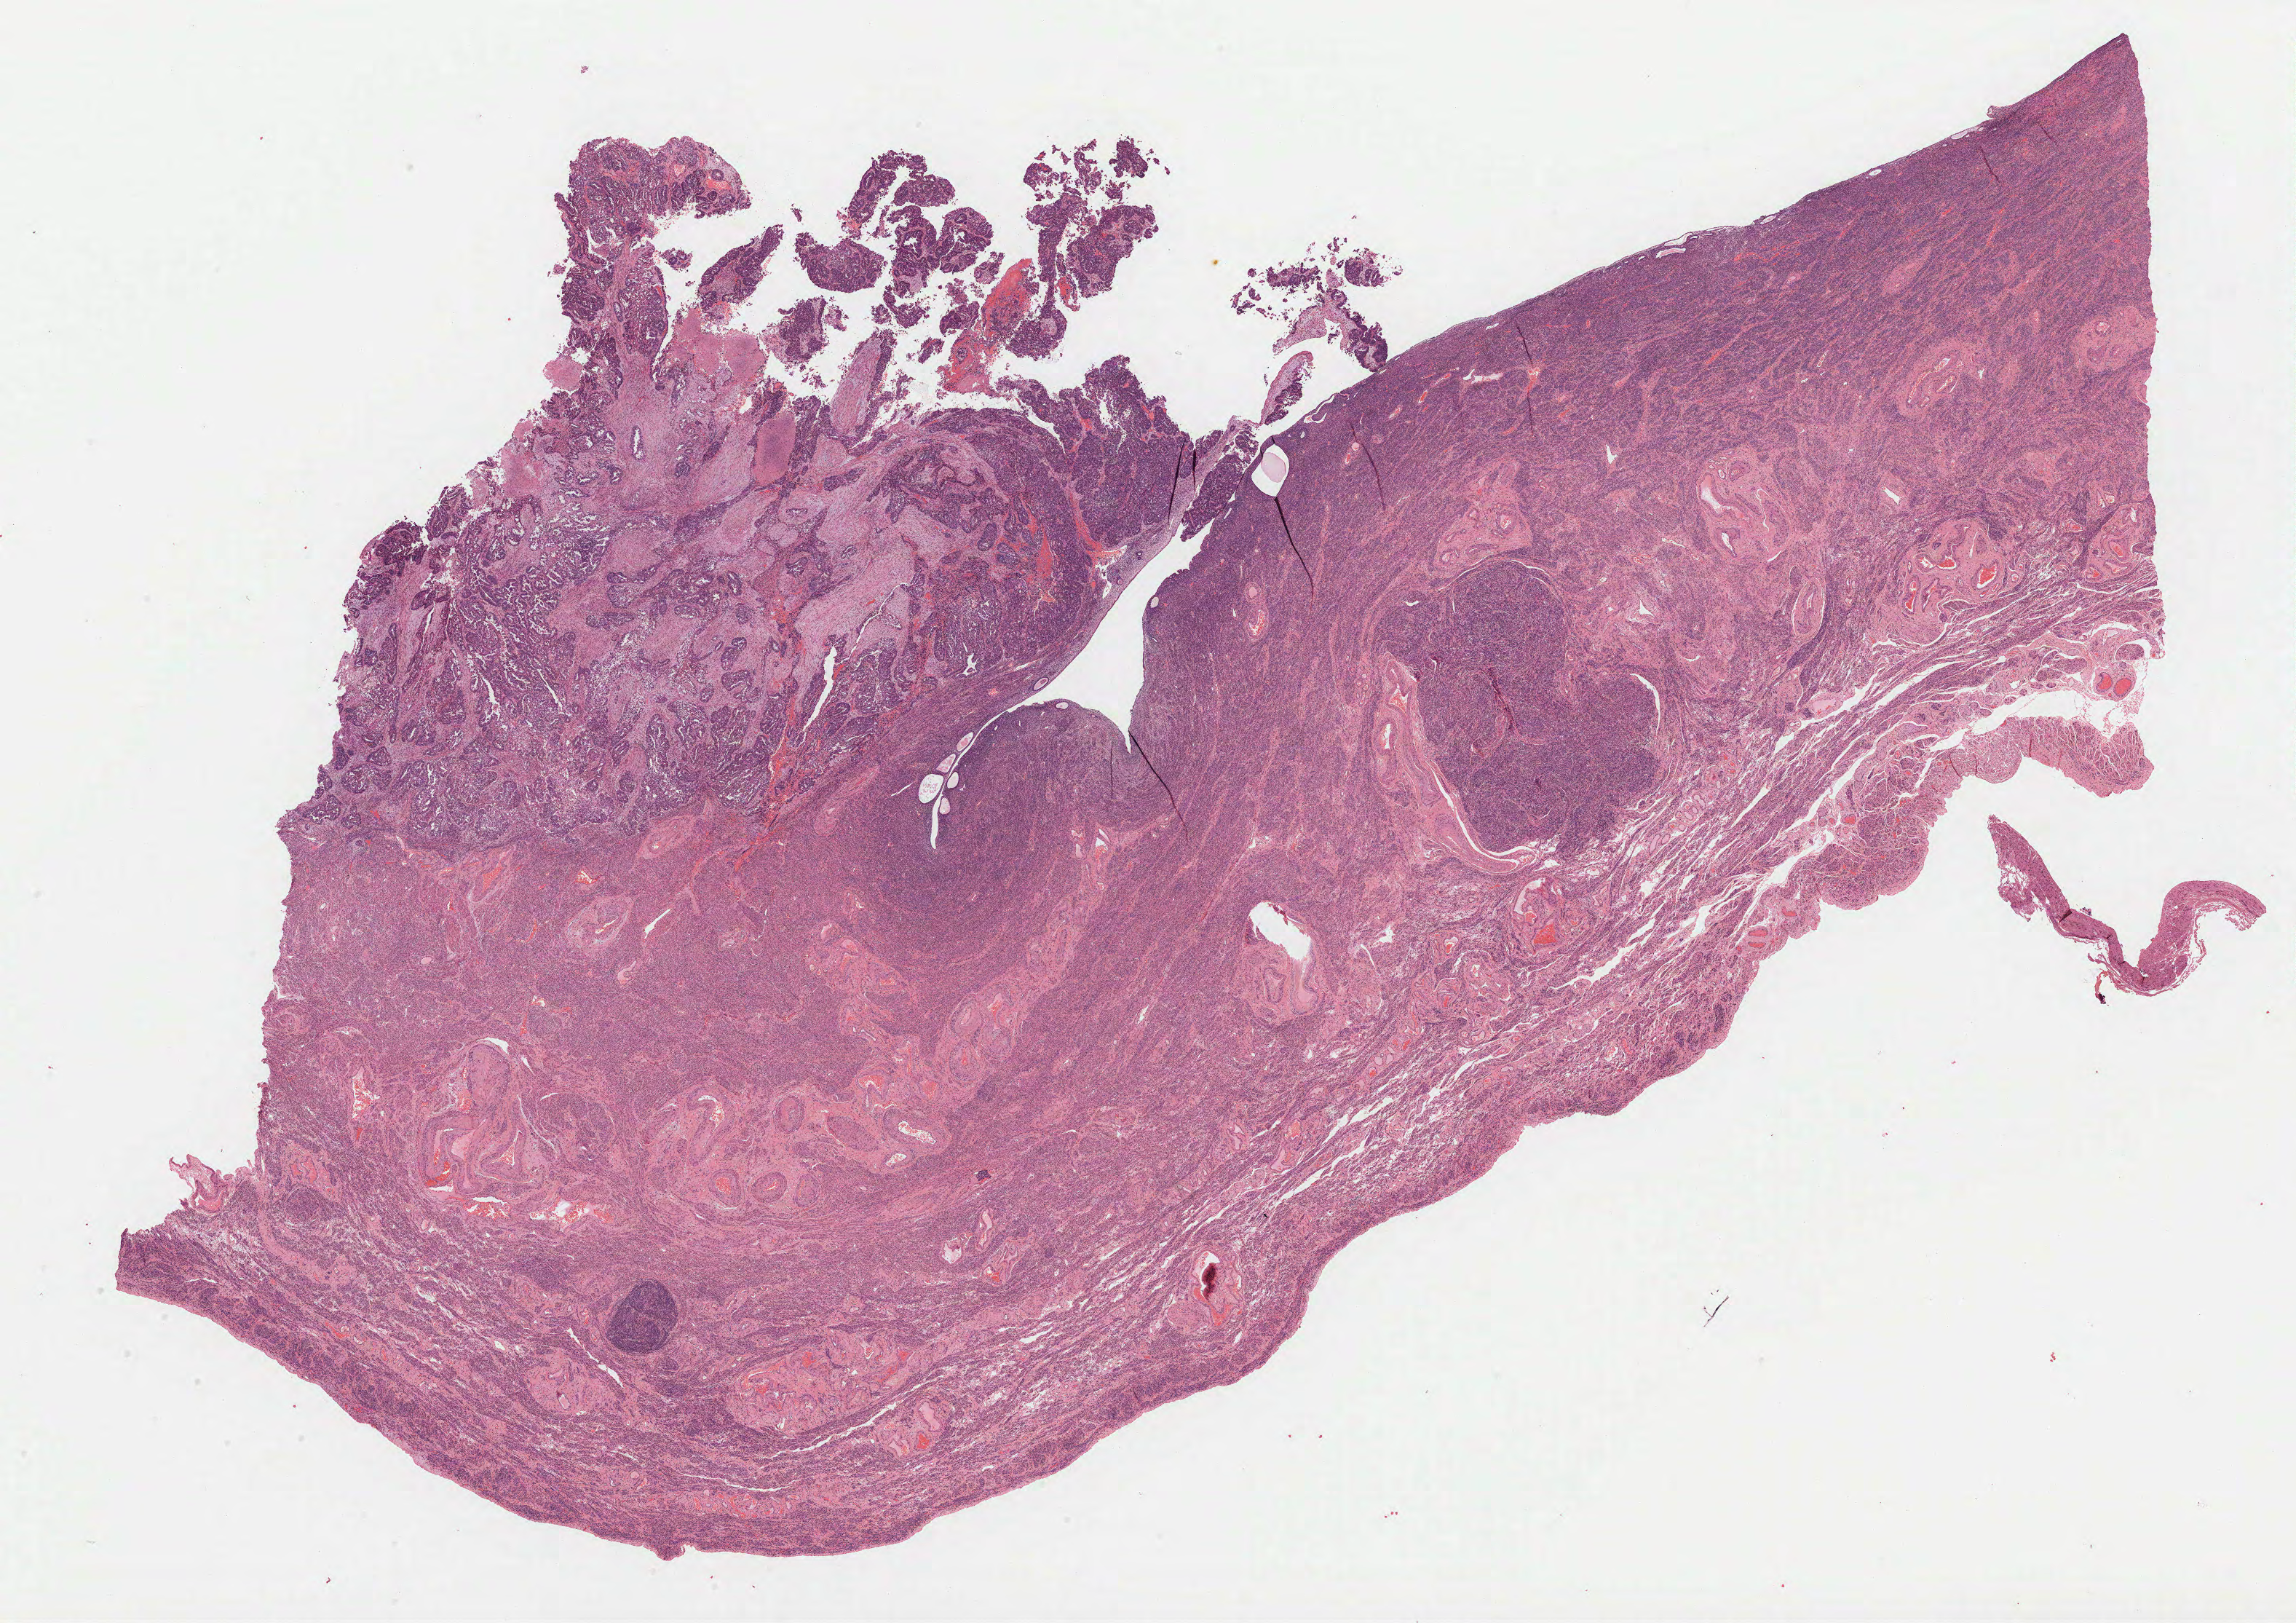
Digitized Hematoxylin and eosin (H&E) stained tissue section (whole slide), a low-resolution overview of the entire scanned area, about 25.4 x 18.0 mm; FFPE section; primary tumour sample from the uterus. Female patient. Histologic grade: G3 (poorly differentiated).
Diagnosis: Serous cystadenocarcinoma, NOS (endometrium). FIGO stage: IA.